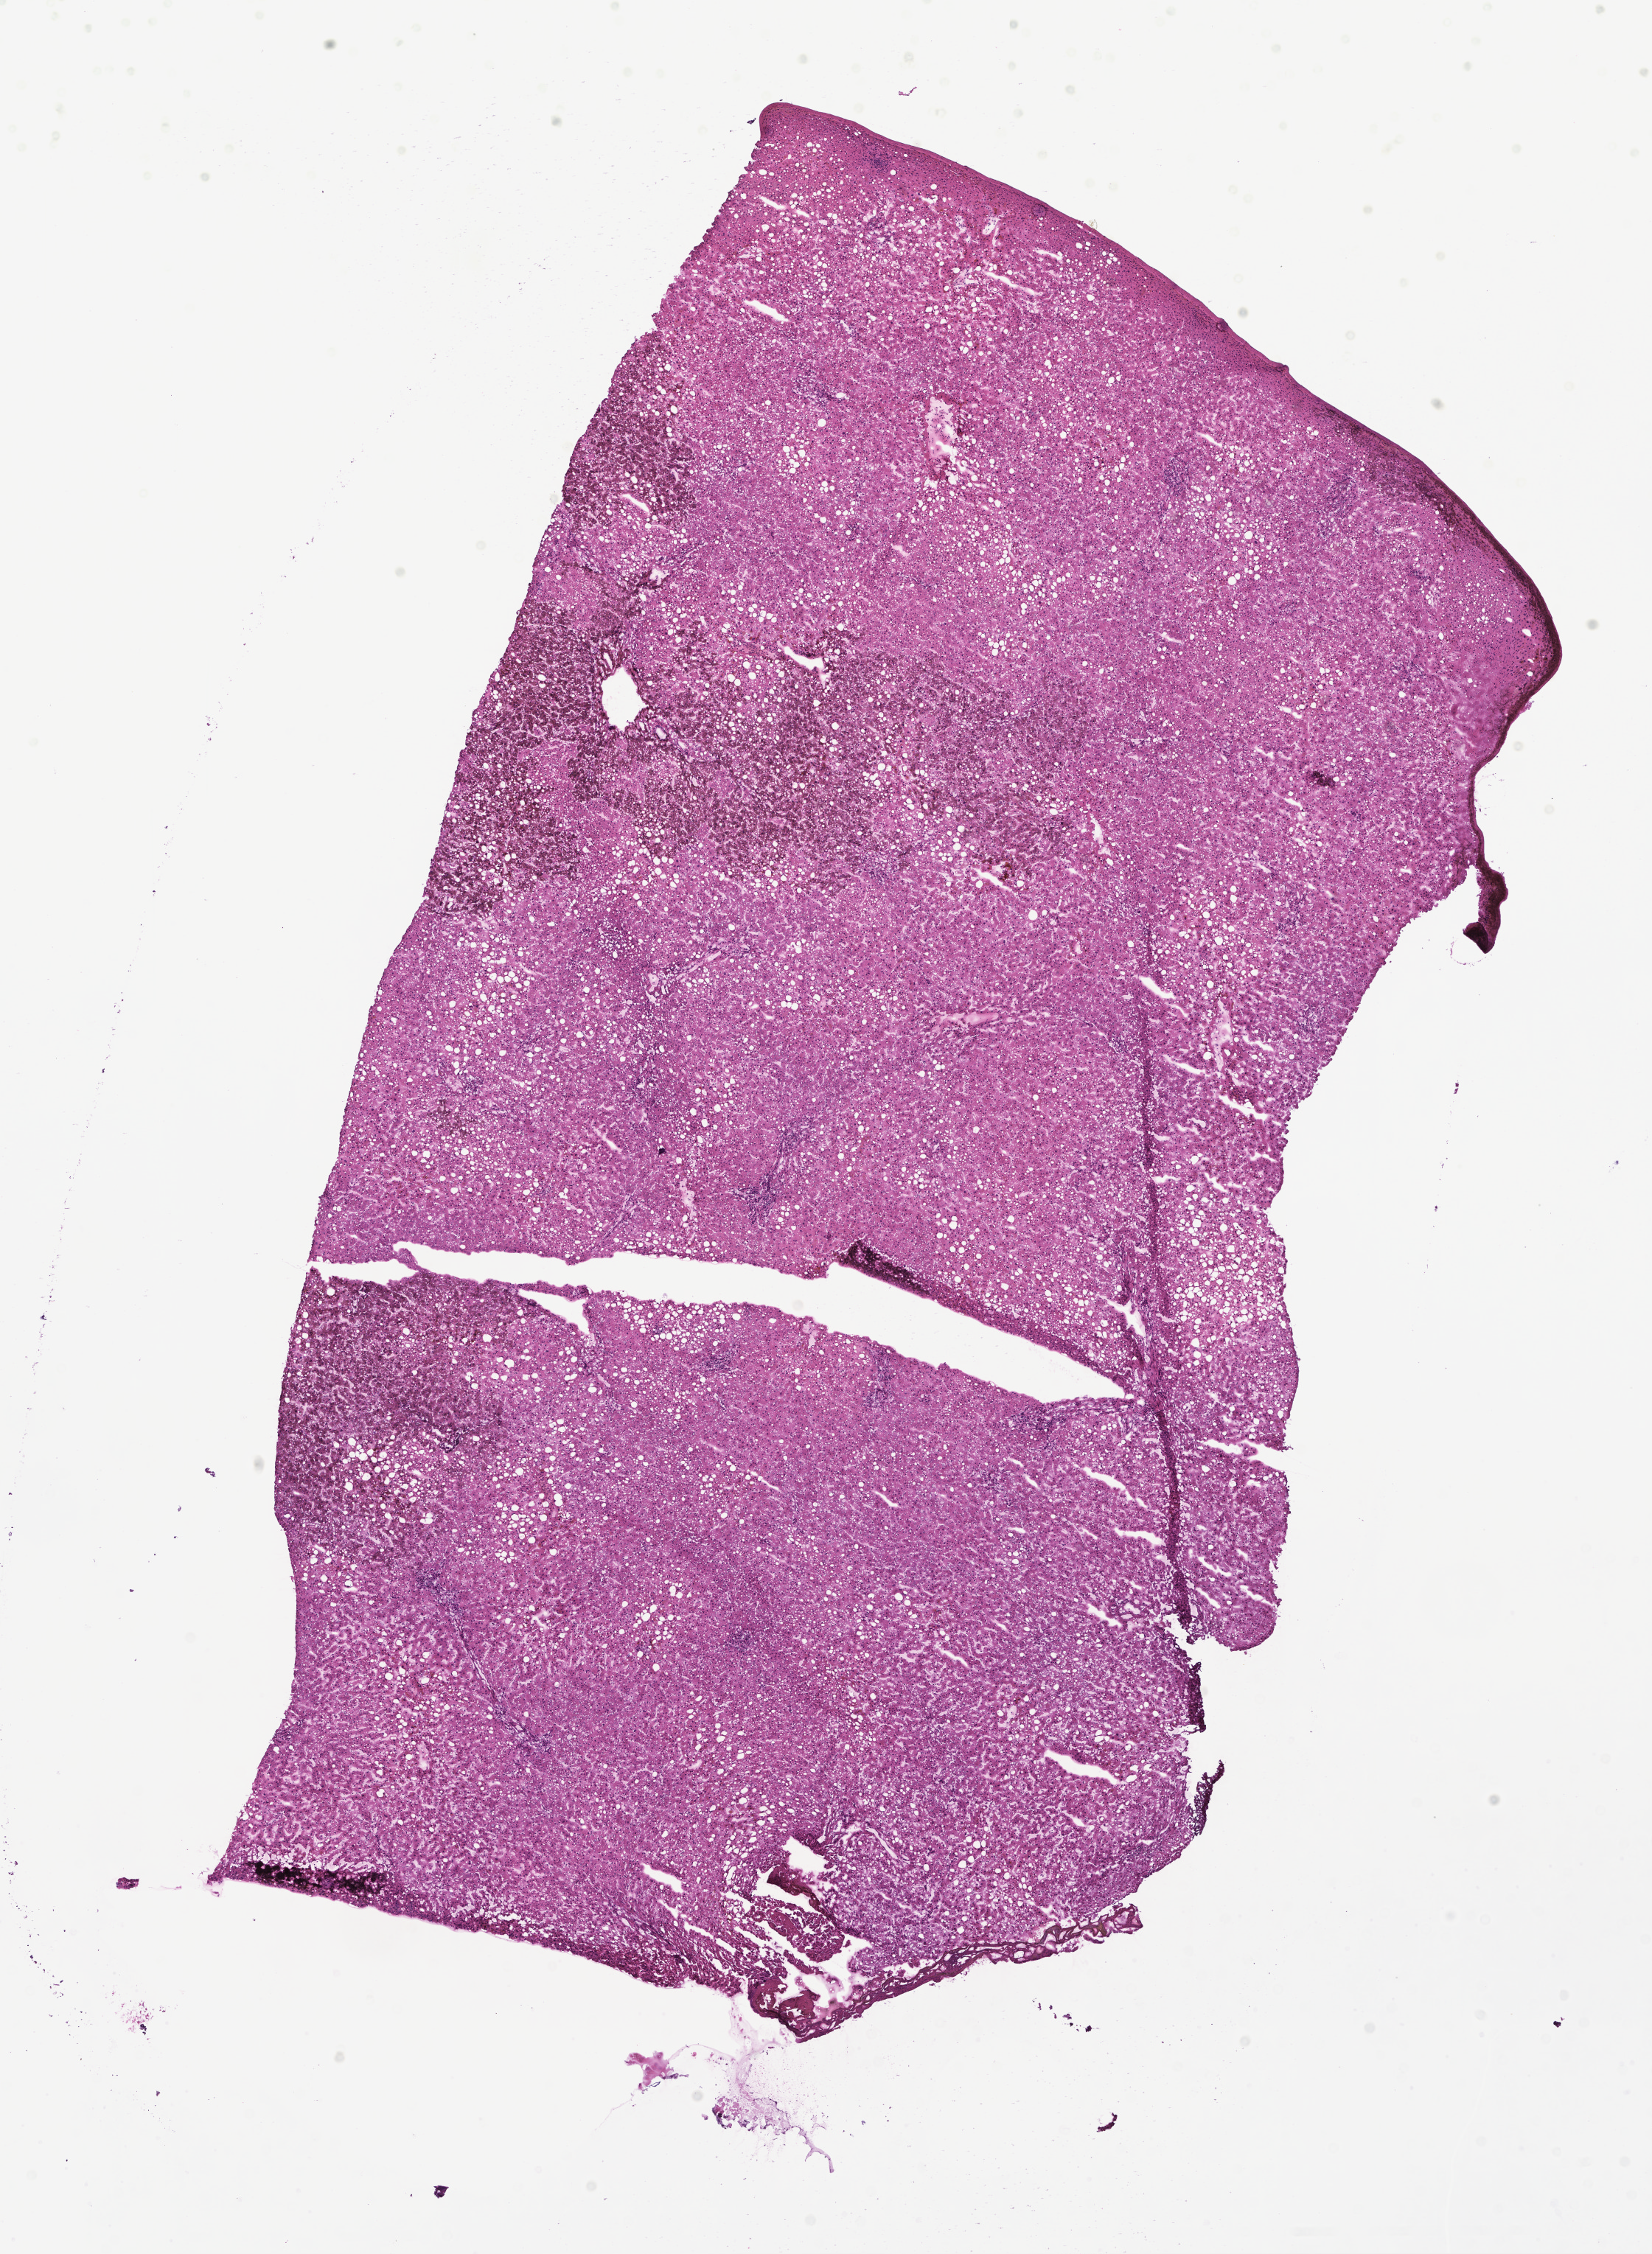
Hematoxylin and eosin (H&E) whole-slide image — whole scanned area (about 9.1 x 12.4 mm) shown as a low-resolution overview; frozen section; non-tumor (normal tissue) sample from a patient with adenocarcinoma, NOS; site: colon. Patient: male, age at initial diagnosis 72 years.
This section: non-tumor tissue sample; the patient's diagnosis is given above. Section: bottom of the tissue portion.